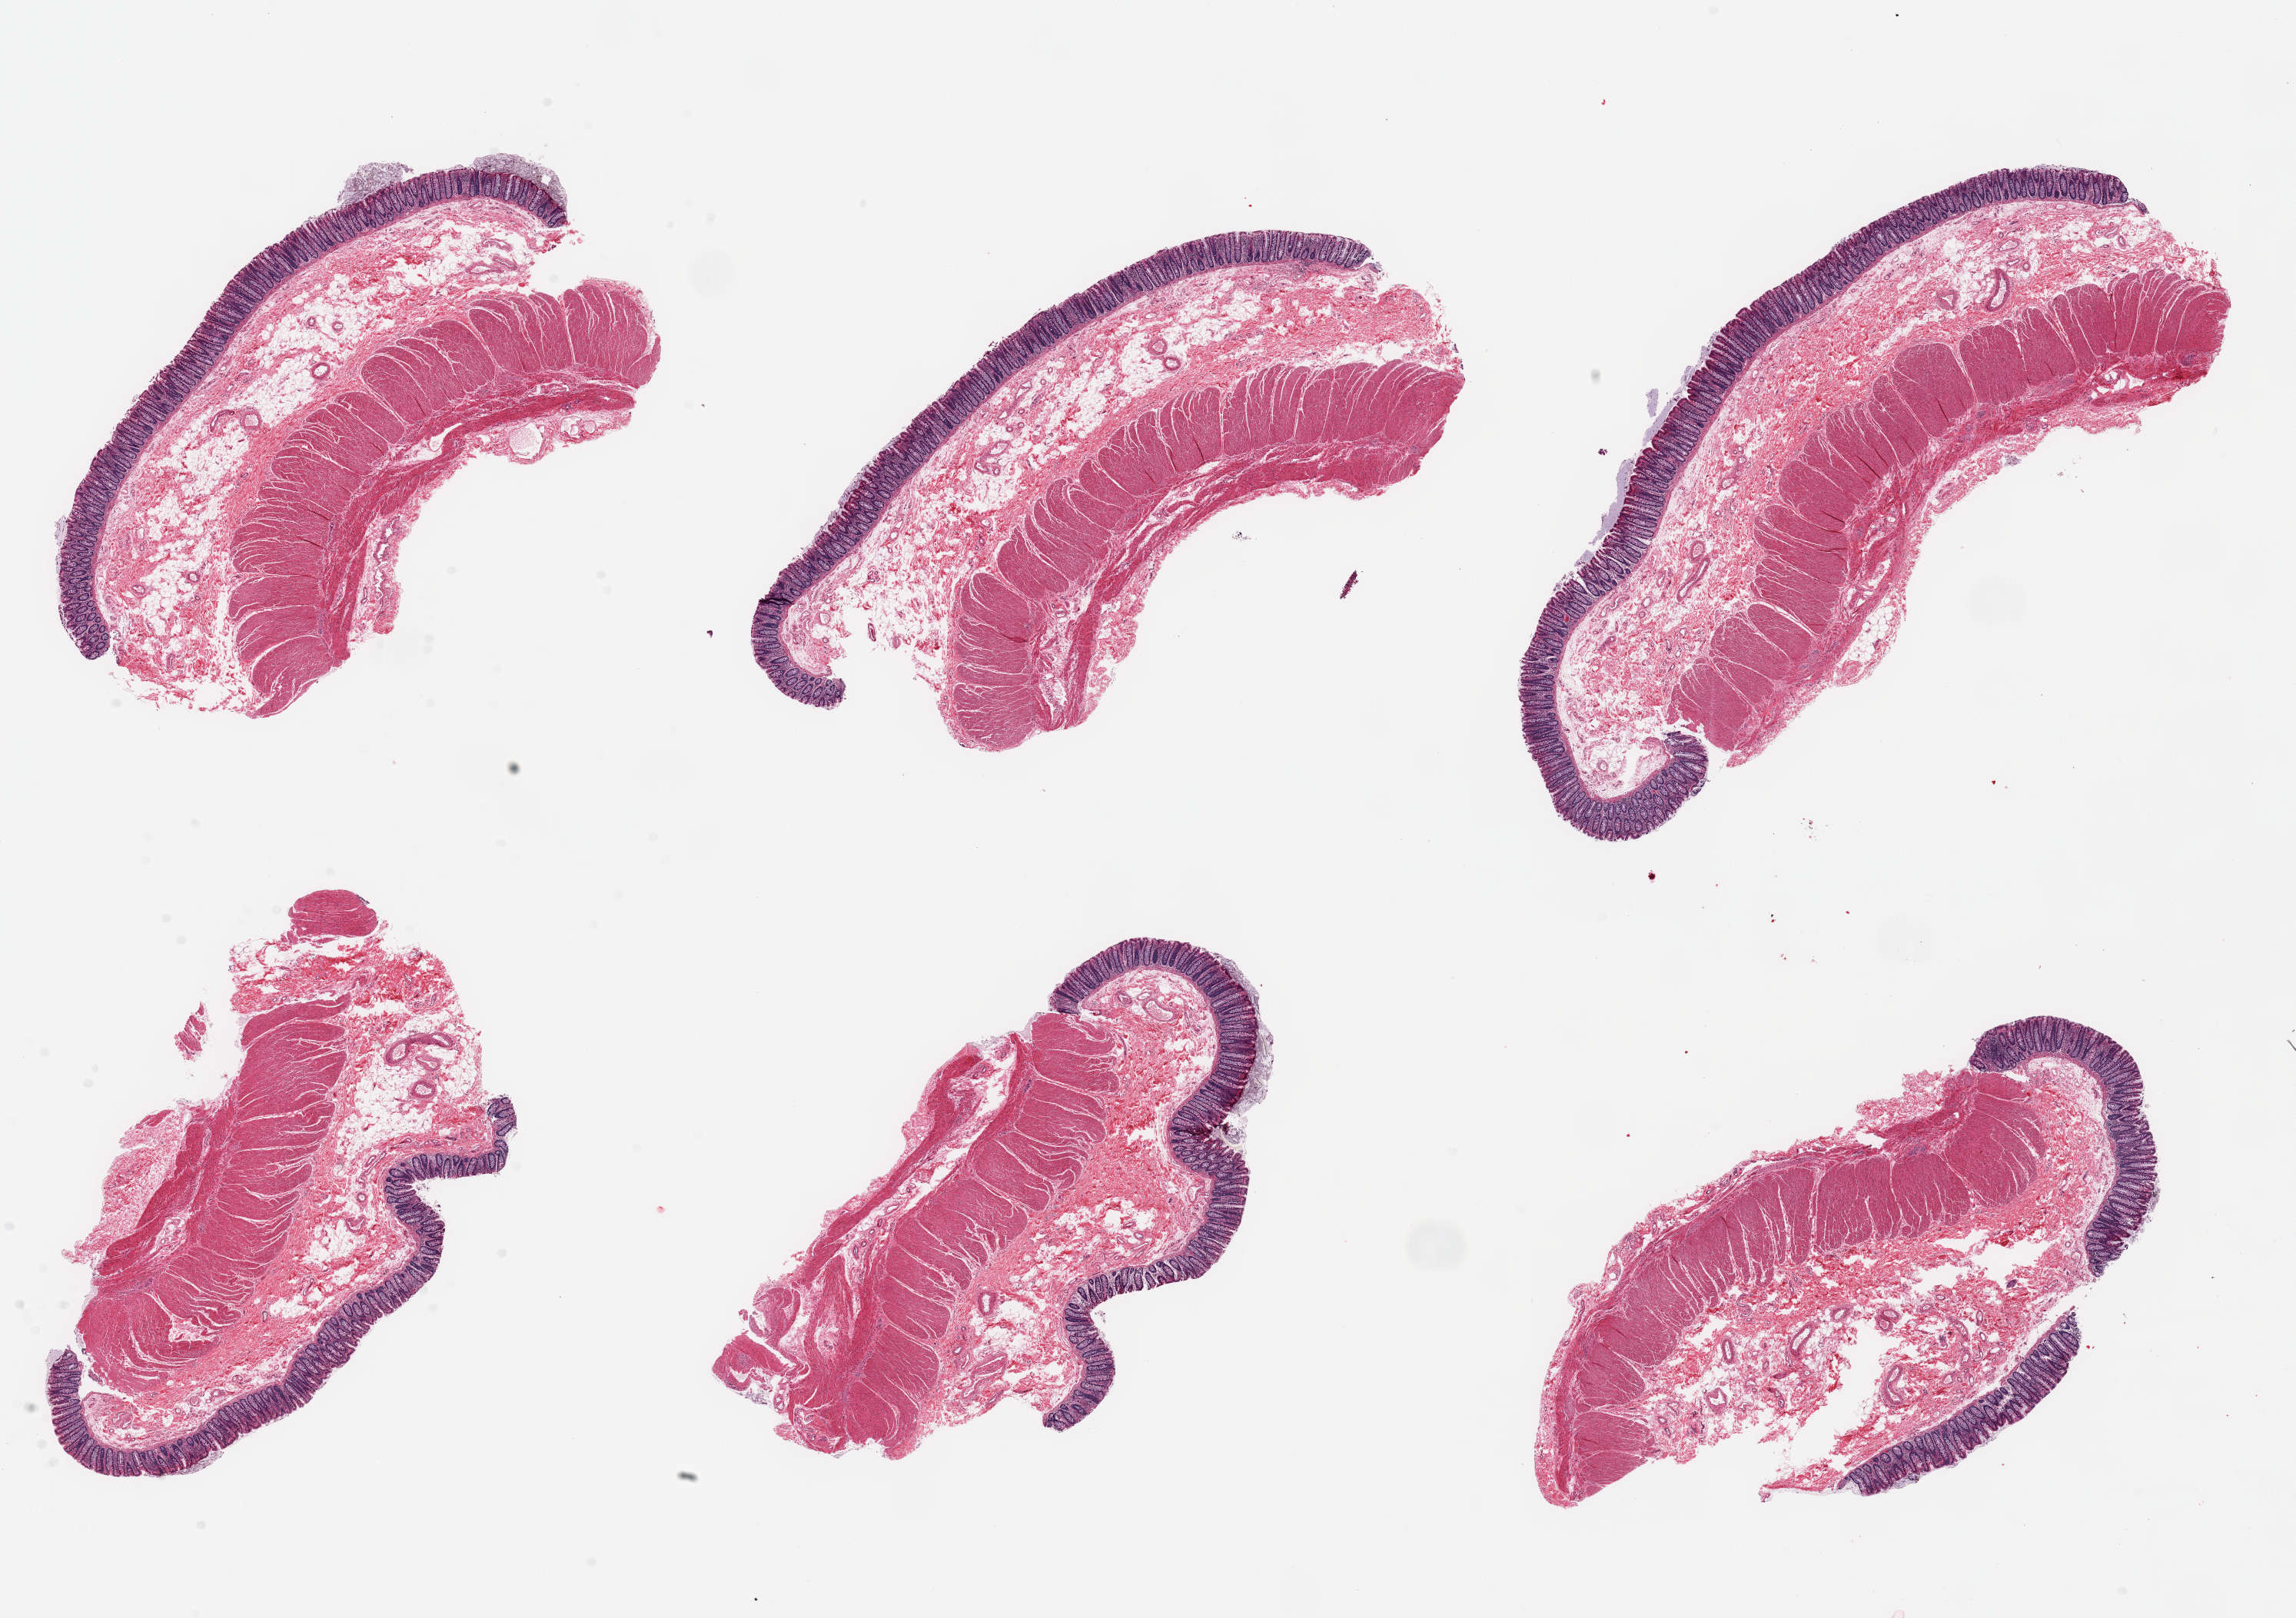
Haematoxylin and eosin whole-slide image, whole scanned area (about 23.6 x 16.6 mm, from a 20x scan) shown as a low-resolution overview. PAXgene-fixed, paraffin-embedded tissue. Sampled site (target tissue): transverse colon. Tissue donor sample. Male donor.
Reviewer comment on this tissue sample: 6 pieces, well fixed mucosa 0.3-0.4mm thick, ~10% thickness.